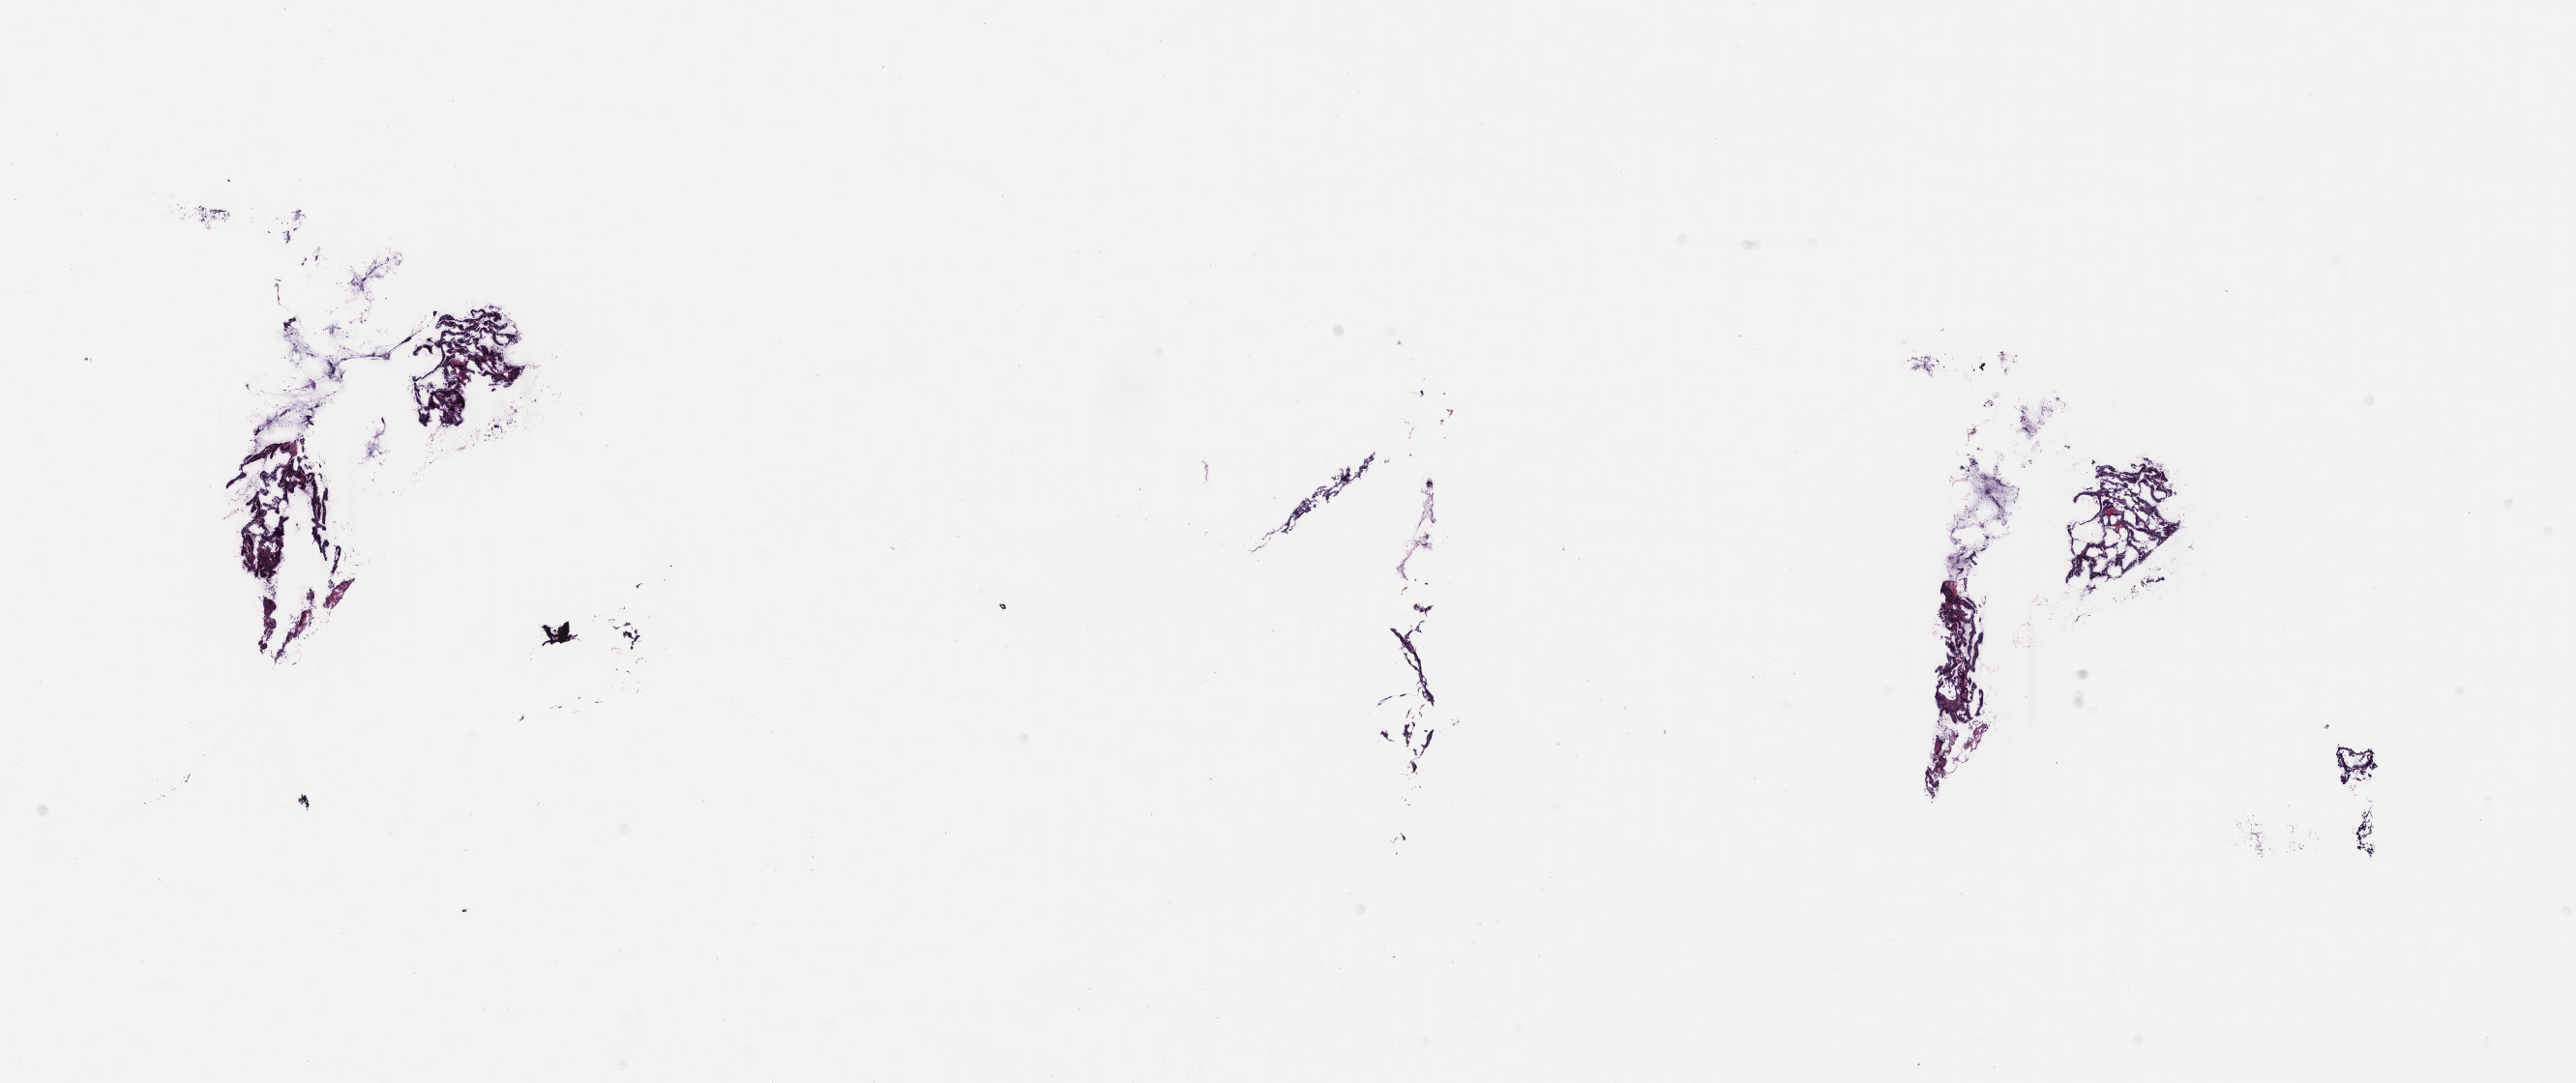
Whole-slide histology image, Hematoxylin and eosin (H&E) stained — shown as a low-resolution overview of the whole scanned area (about 21.2 x 8.9 mm, slide scanned at 40x). Frozen section. Primary tumour sample from the uterus. Female patient; age at initial diagnosis 69 years. Histologic grade: G1 (well differentiated). Slide review estimates, as recorded: tumour cells 90%, tumour nuclei 90%, normal cells 0%, stromal cells 10%, necrosis 0%. Infiltration values recorded for this section: lymphocyte infiltration 20%, monocyte infiltration 0%, neutrophil infiltration 5%.
FIGO stage: IB. Histologic diagnosis: Endometrioid adenocarcinoma, NOS (fundus uteri).